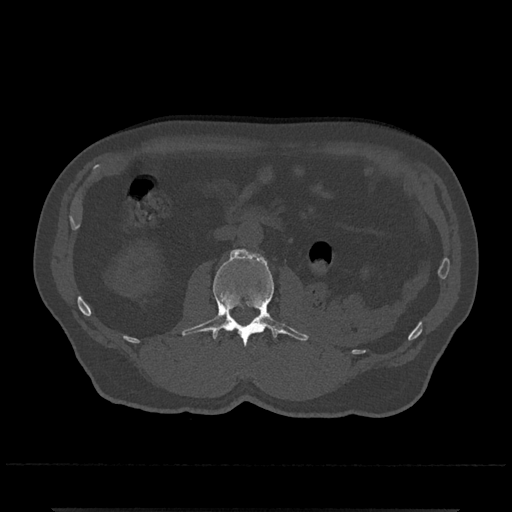
CT including the spine, one axial slice; bone window (W 1800 / L 400 HU); 0.5 mm slice thickness; 512 × 512 image matrix, field of view 393 × 393 mm. Patient: male, 67 years. Case-level facts recorded for this patient, not image findings: primary cancer: prostate.
Outlined on this slice (semi-automatically segmented with operator editing):
- L2 vertebra: box from (x=182, y=249) to (x=309, y=346) px